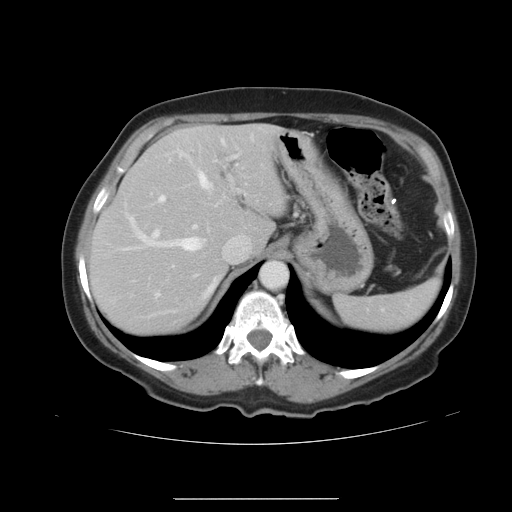
Contrast-enhanced abdominal CT, one axial slice; position 28 of 41 along the scan axis; 120 kVp; intravenous contrast given; soft-tissue window (W 400 / L 40 HU); 5 mm slice thickness; 512 × 512 image matrix, field of view 381 × 381 mm. Female patient, age 63 years. From the clinical record (not read from this slice): diagnosis: colorectal cancer liver metastases, imaged before liver resection; multiple liver metastases: yes.
Annotated regions visible in this slice (expert manual segmentation):
- hepatic veins: bounding box <120,140,224,292> (left, top, right, bottom; pixels)
- liver: <90,125,287,337>
- planned liver remnant (the part of the liver to remain after resection): <90,125,287,337>
- portal vein (with intrahepatic branches): <153,154,239,295>